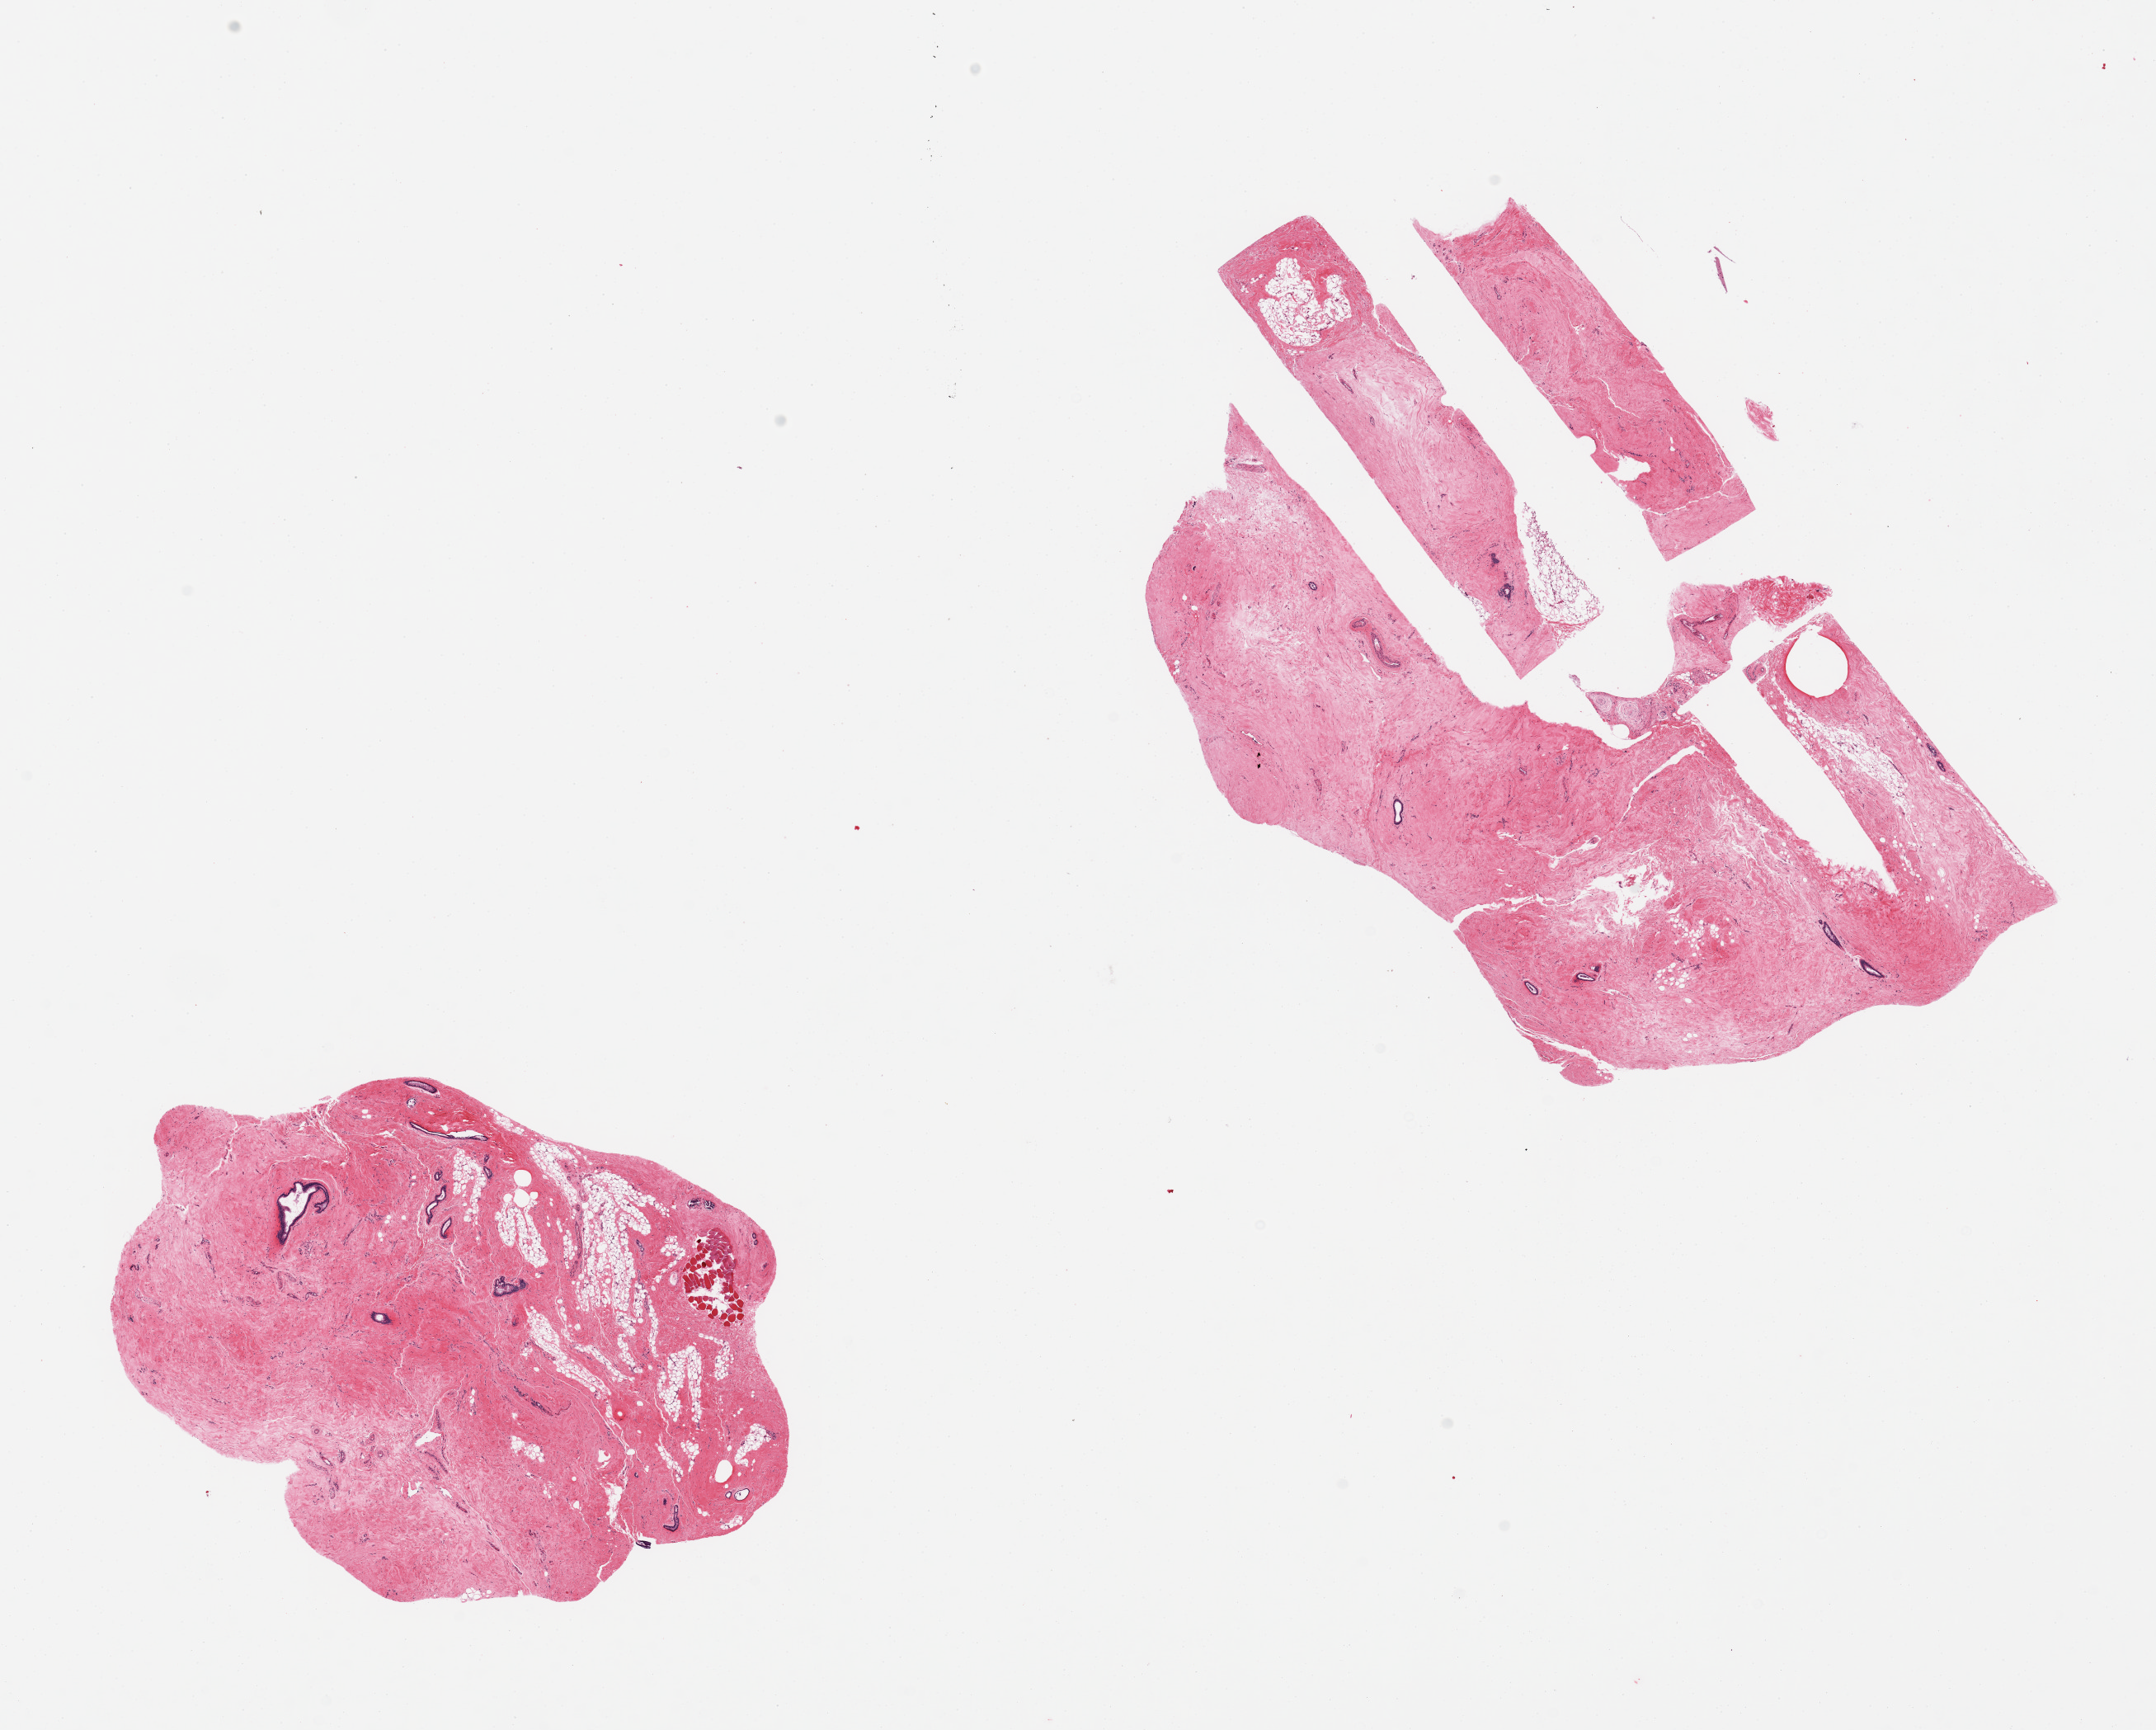
Digitized haematoxylin and eosin-stained section, whole scanned area (about 20.7 x 16.6 mm) shown as a low-resolution overview. PAXgene-fixed paraffin-embedded (PFPE) section. Section of breast (target tissue). Tissue donor sample.
Reviewer comment on this tissue sample: 2 pieces, gynecomastoid stromal hyperplasia, rare ductal elements.